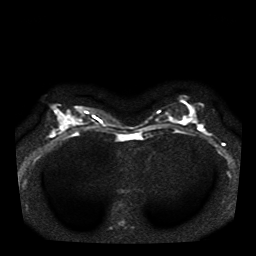
Breast MRI, one axial slice; position 19 of 41 along the scan axis; diffusion-weighted series; image 2 of 4 stored at this slice position (different b-values; order by instance number); 1.5 T; 5 mm slice thickness; 256 × 256 image matrix, field of view 330 × 330 mm. Female patient.
Outlined on this slice (manually delineated by an expert):
- tumour on diffusion-weighted imaging: bounding box [x1, y1, x2, y2] px = [192, 117, 196, 121]